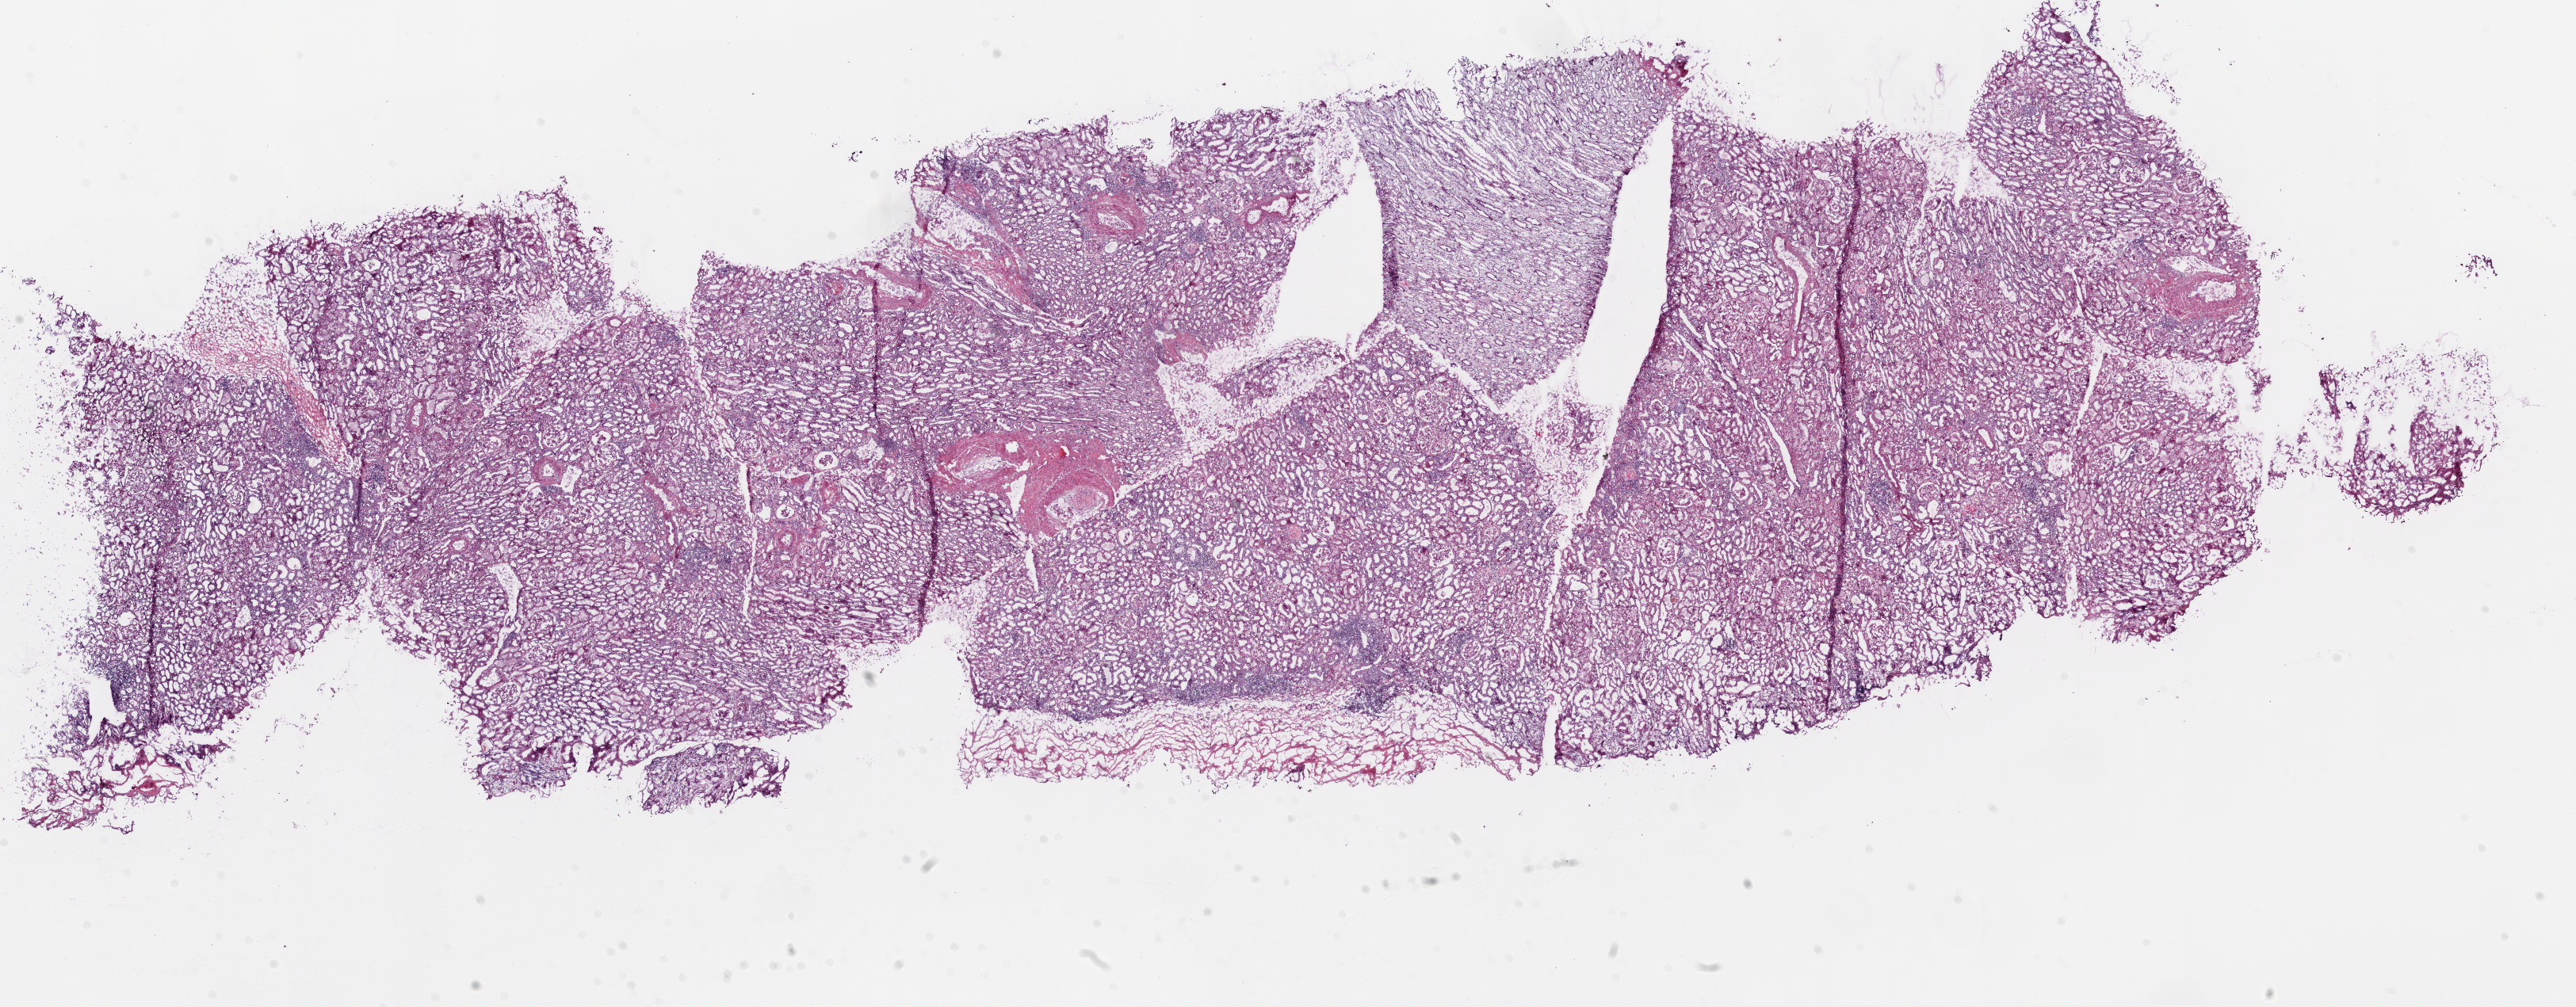
H&E whole-slide image — a low-resolution overview of the entire scanned area, about 26.1 x 10.2 mm (slide scanned at 20x), frozen section from the top of the tissue portion, kidney, solid tissue normal (non-tumour tissue) sample. Patient: male, age at initial diagnosis 48 years.
• this section: solid tissue normal sample (biorepository sample class)
• patient diagnosis: Clear cell adenocarcinoma, NOS